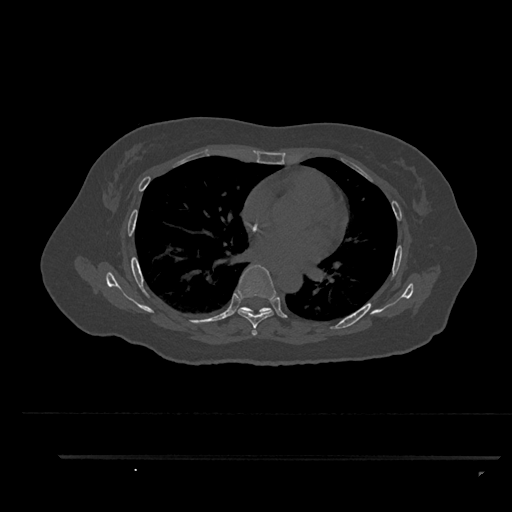
CT including the spine, one axial slice; slice 543 of 797 in the series (ordered by position); 120 kVp; bone window (W 1800 / L 400 HU); 0.5 mm slice thickness; 512 × 512 image matrix, field of view 408 × 408 mm. Female patient, age 44 years. From the clinical record (not read from this slice): primary cancer: renal; vertebrae with lytic lesions (as recorded): L1.
Annotated regions visible in this slice (semi-automatic segmentation, software-assisted and operator-edited):
- T6 vertebra: bounding box <235,264,276,336> (left, top, right, bottom; pixels)
- T7 vertebra: <239,307,273,315>